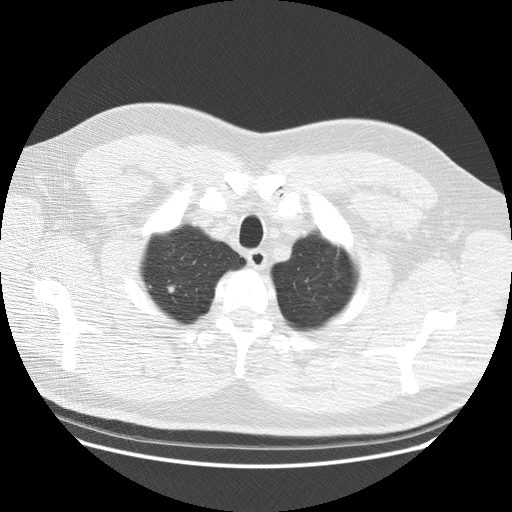
Low-dose screening chest CT, one axial slice; 120 kVp; lung window (W 1500 / L -600 HU); 2.5 mm slice thickness; 512 × 512 image matrix, field of view 389 × 389 mm.
Structures marked on this image (expert manual segmentation):
- lesion 1 (tumor, upper lobe of right lung): bounding box <167,285,181,293> (left, top, right, bottom; pixels)